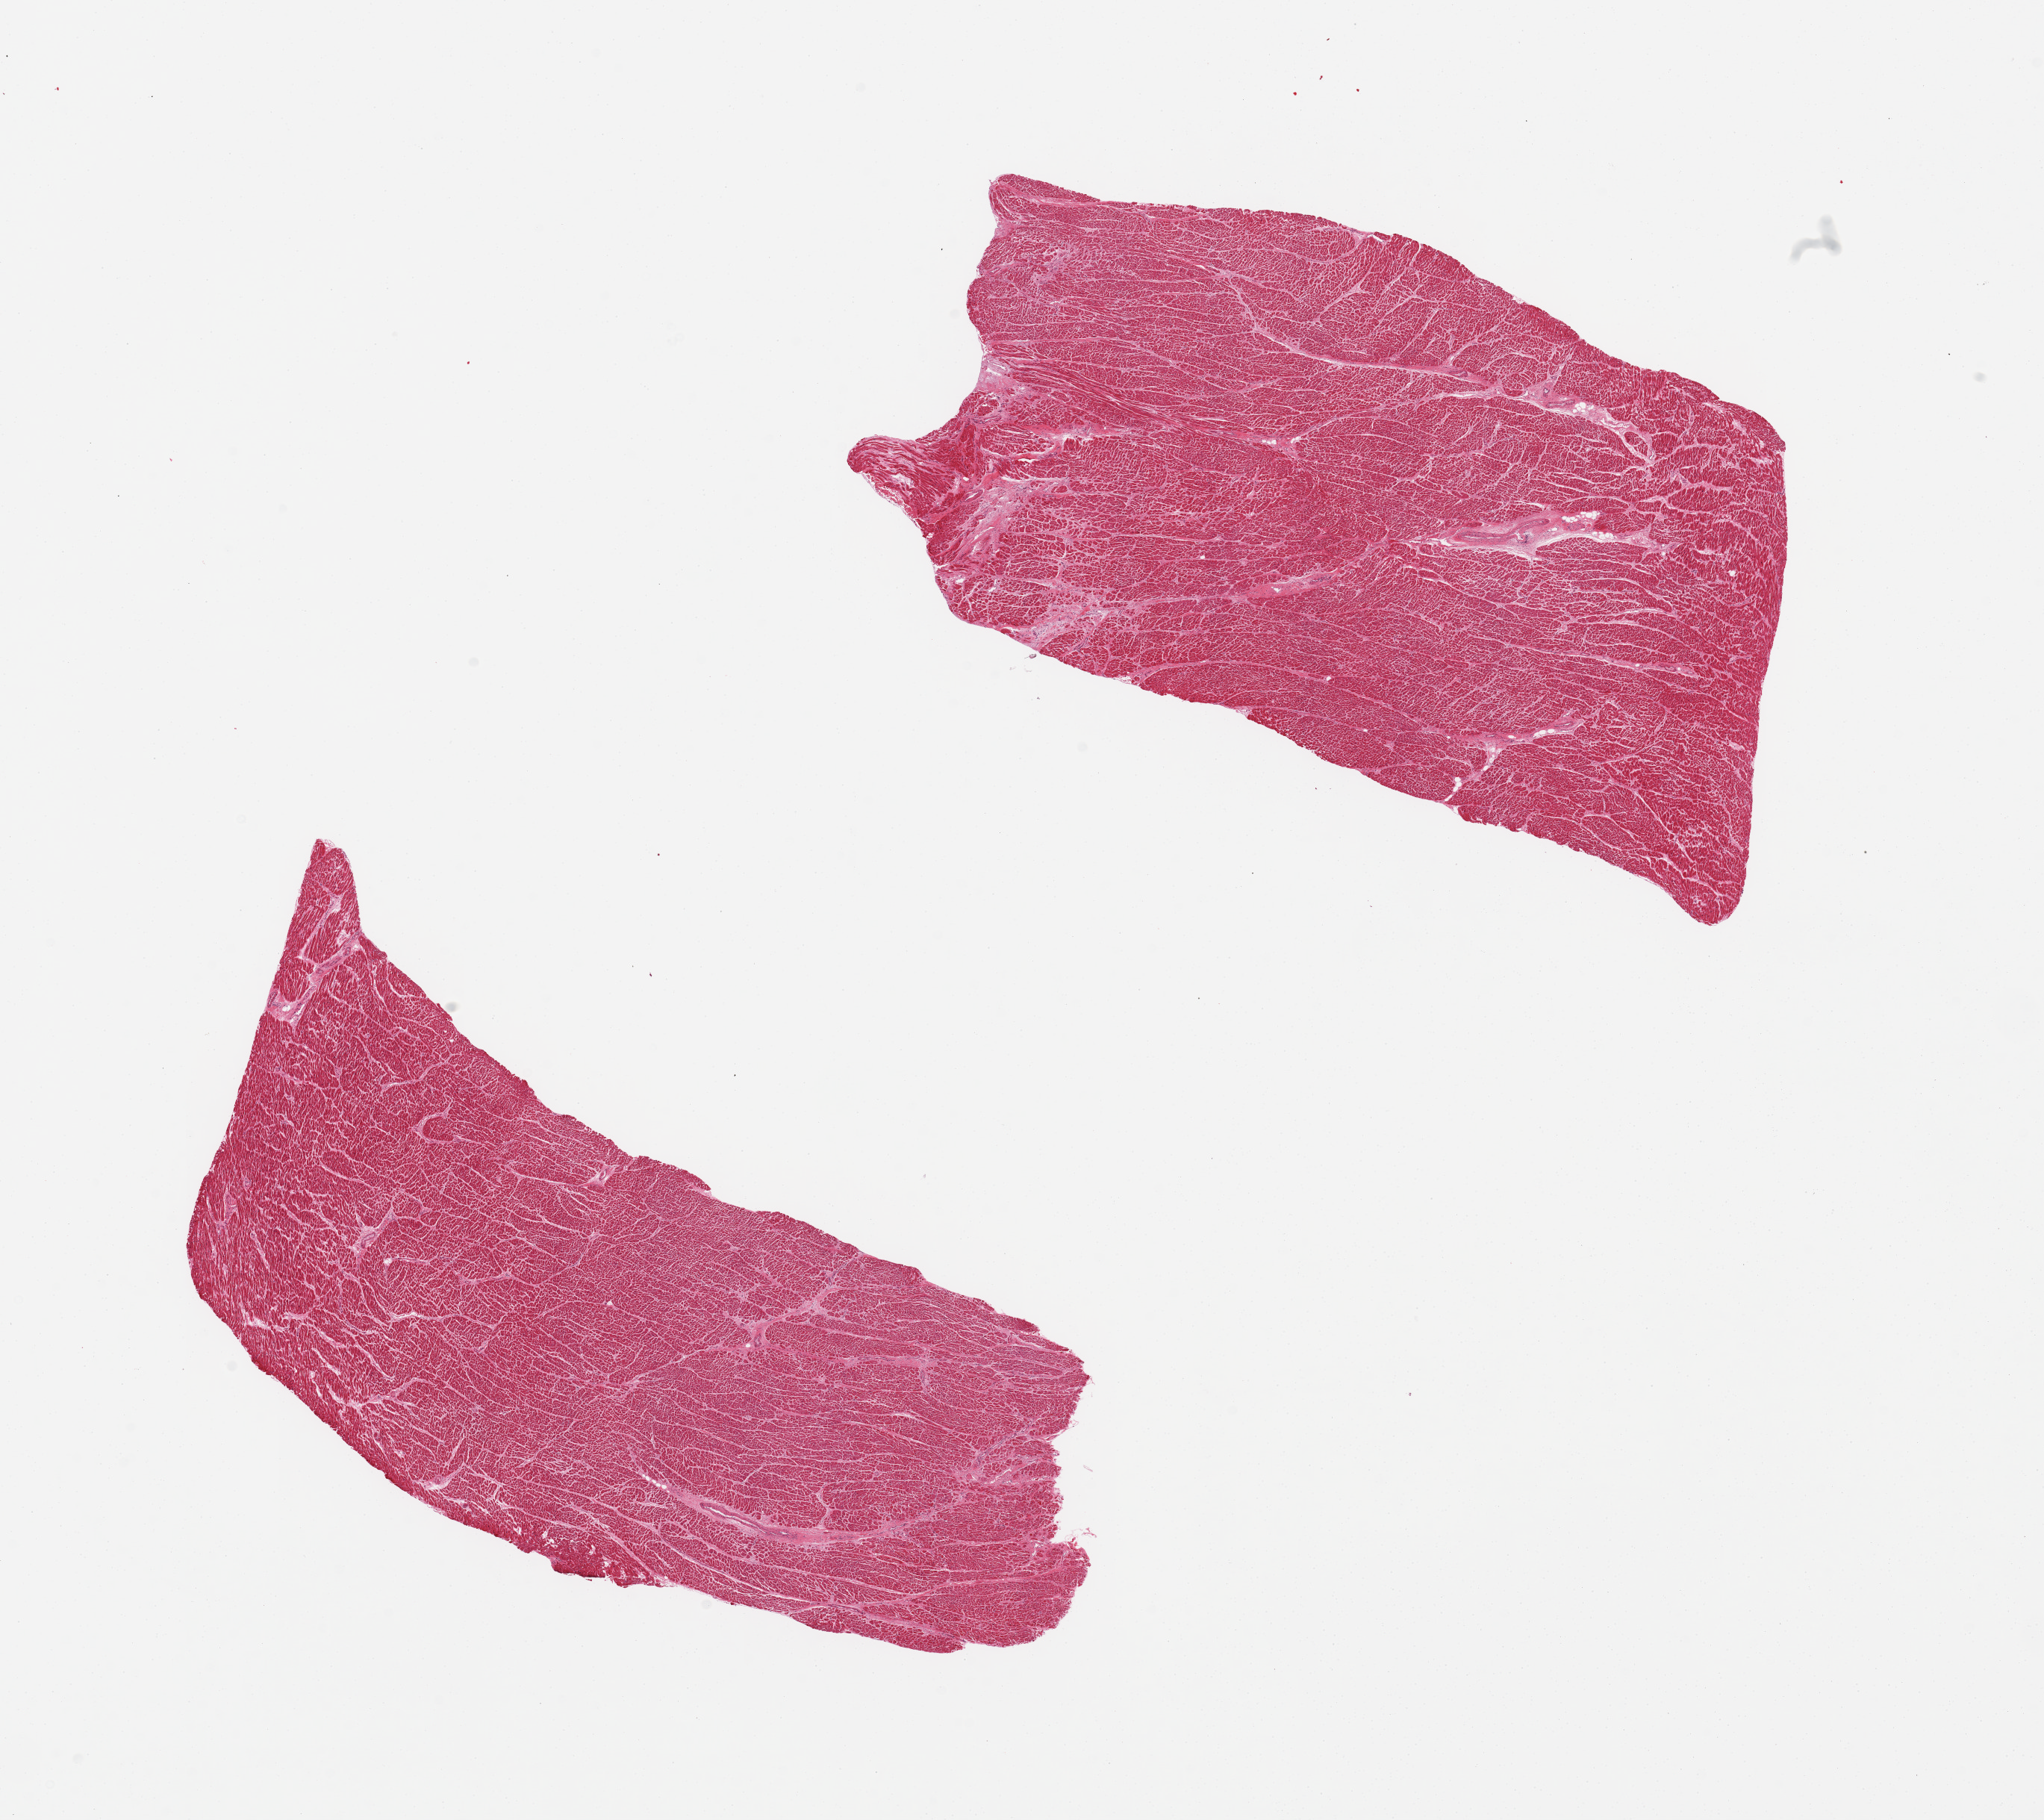
Digitized H&E-stained section, shown as a low-resolution overview of the whole scanned area (about 21.7 x 19.3 mm, acquisition: 20x scan), PAXgene-fixed, paraffin-embedded tissue, target tissue: heart, donor tissue sample. Donor: male.
• reviewer comment on this tissue sample: 2 pieces, patchy interstititial fibrosis, several microinfqrcts noted